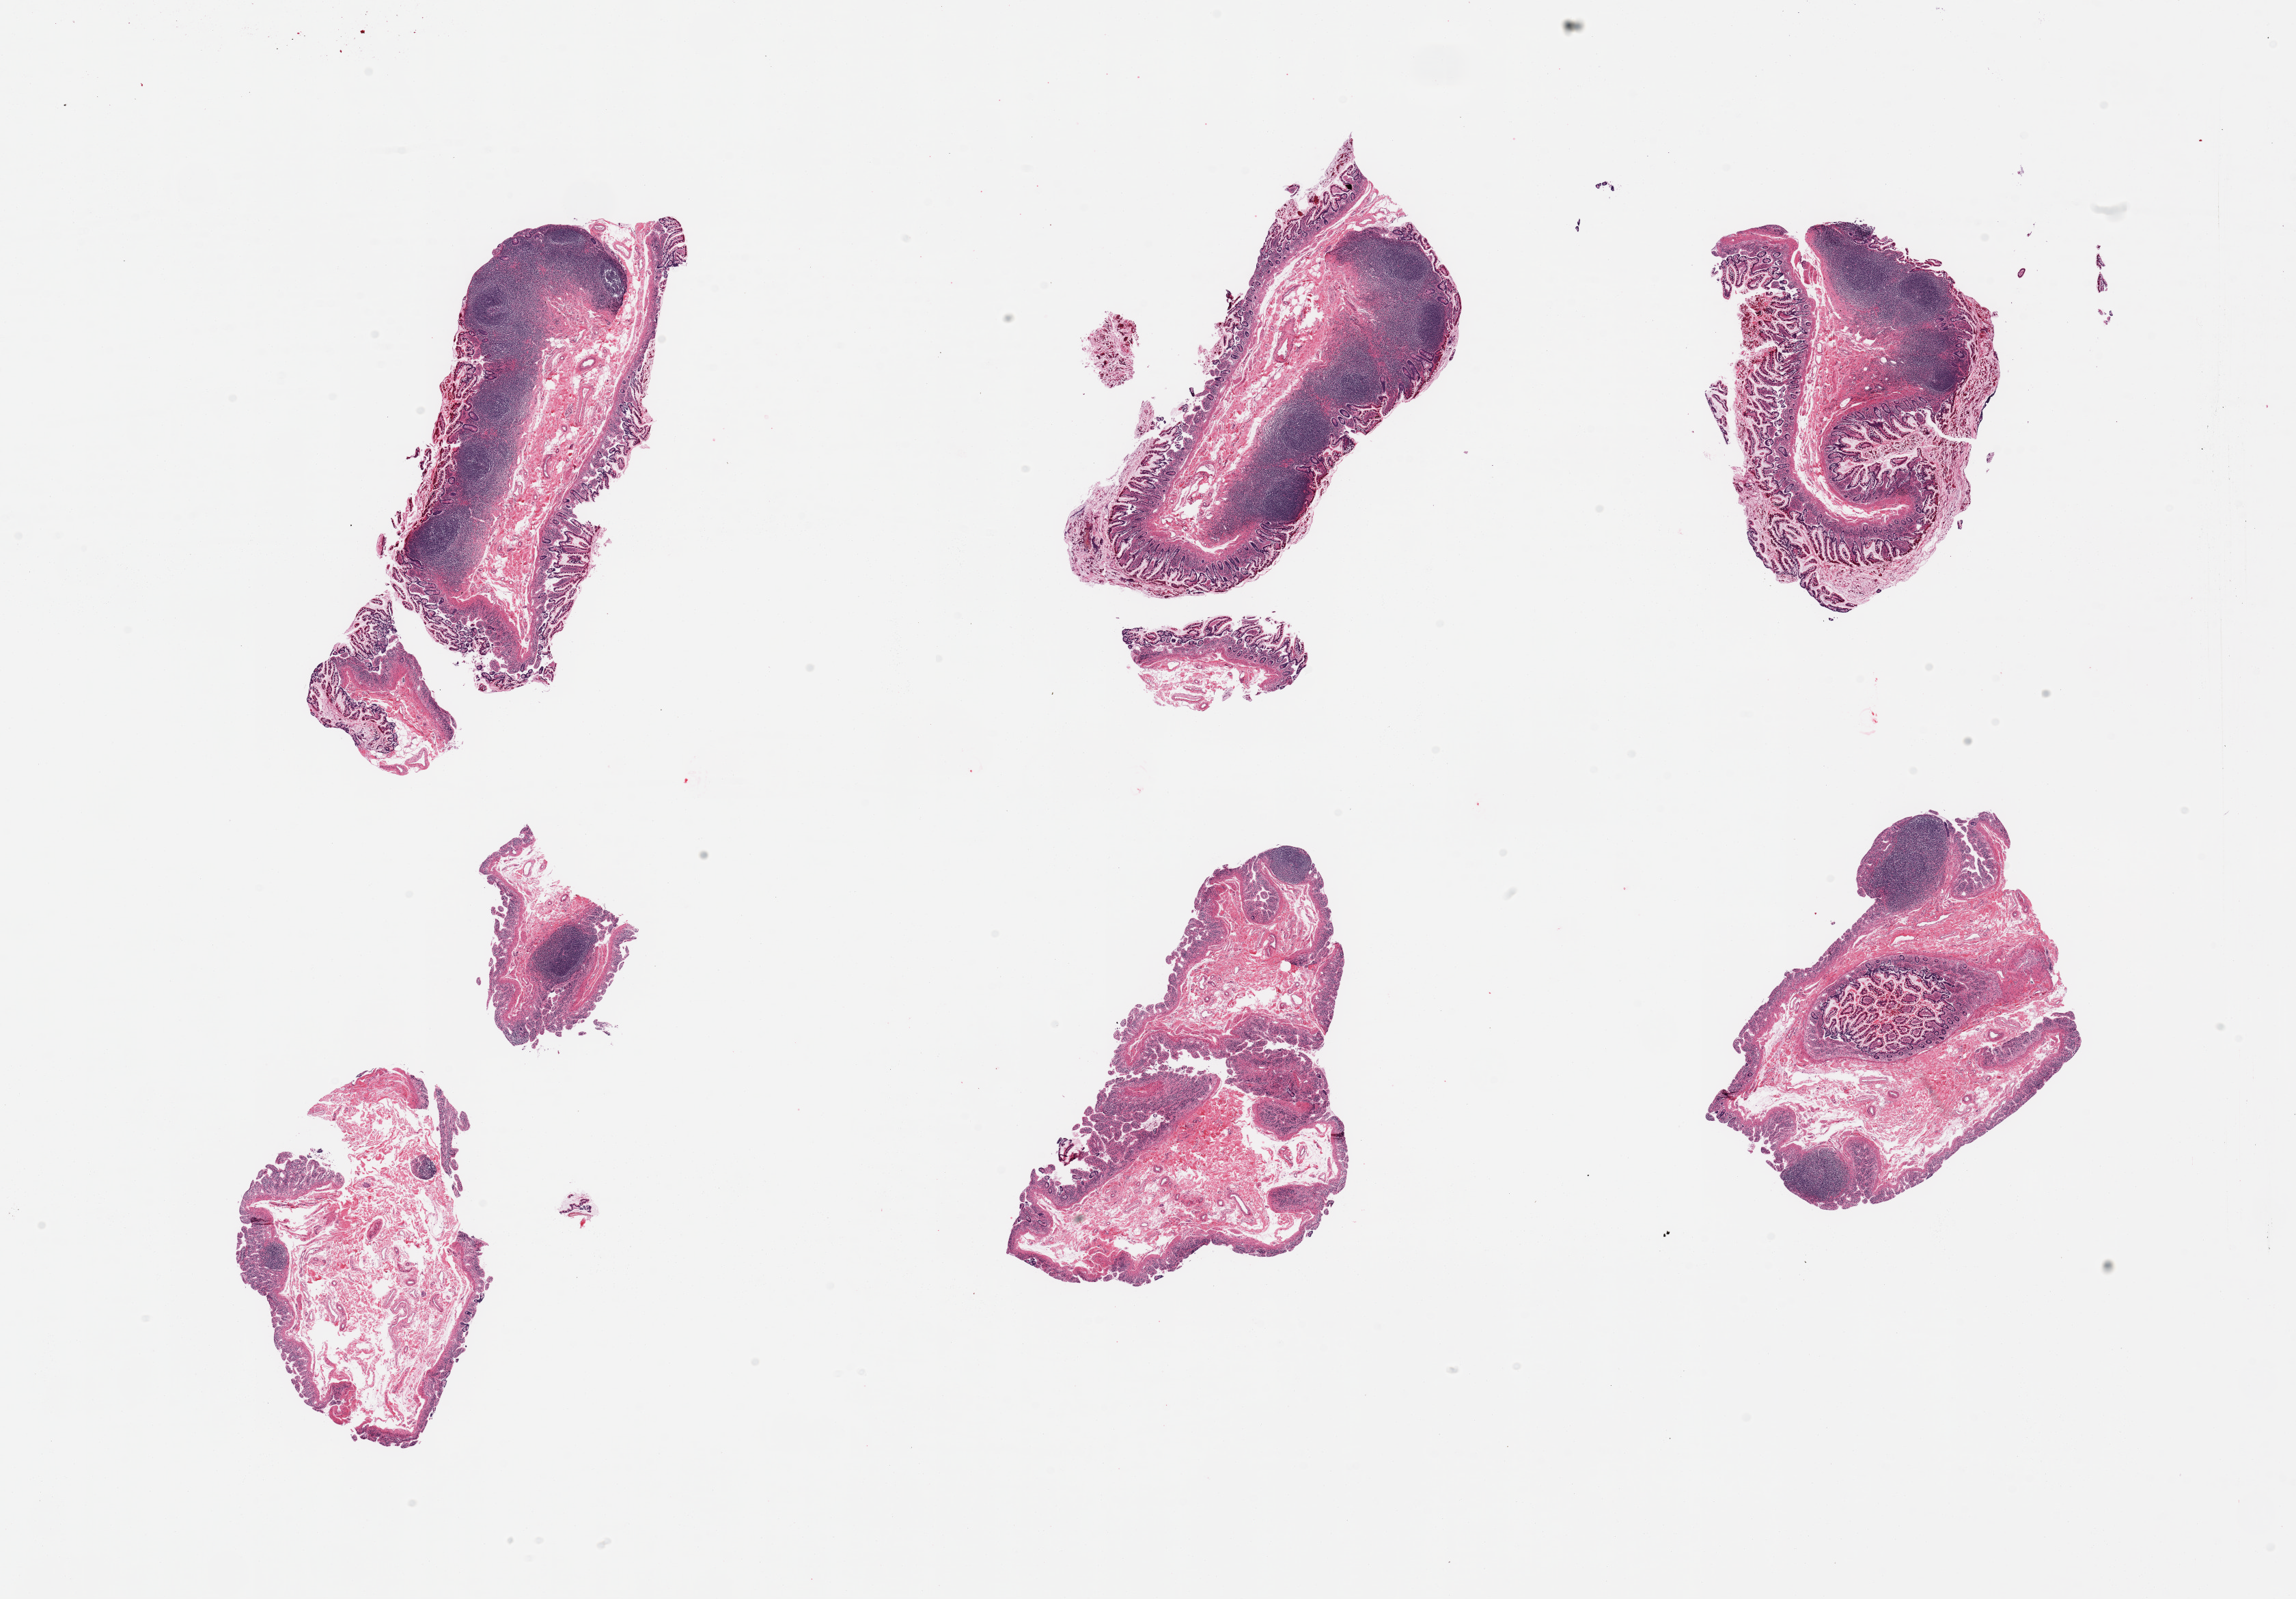
Hematoxylin and eosin (H&E) whole-slide image, brightfield, shown as a low-resolution overview of the whole scanned area (about 26.6 x 18.5 mm, from a 20x scan), PAXgene-fixed, paraffin-embedded tissue, target tissue: ileum, tissue donor sample. Donor: male.
Reviewer comment on this tissue sample: 6 pieces; mucosa and submucosa with good lymphoid component.